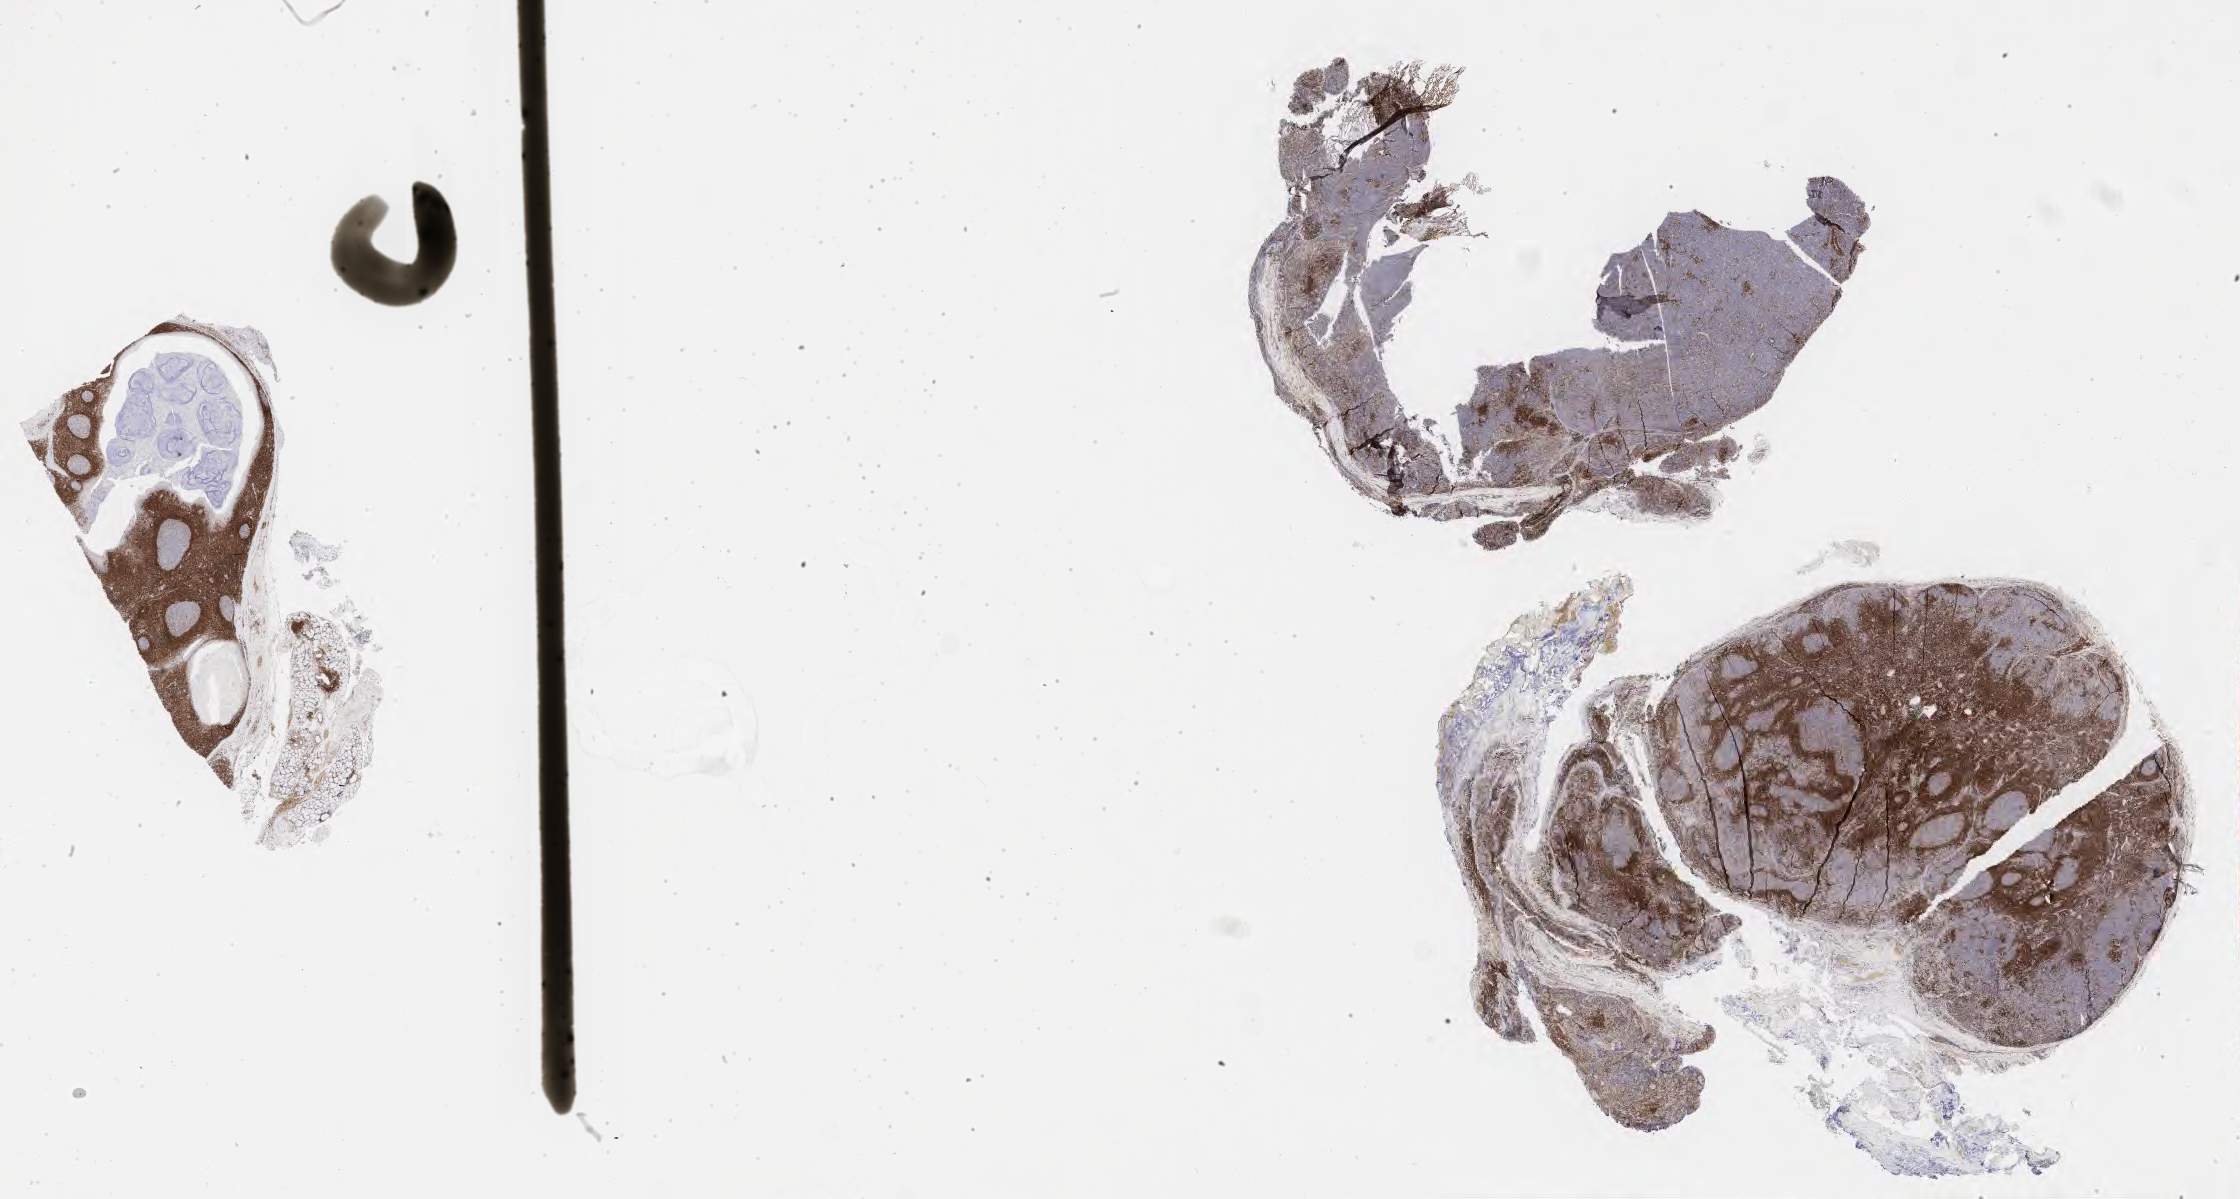
Immunohistochemistry (IHC) whole-slide image stained for BCL2, whole scanned area (about 36.2 x 19.4 mm) shown as a low-resolution overview. Tumor tissue. Patient: male, aged 25.
Histologic diagnosis: Burkitt lymphoma, NOS.